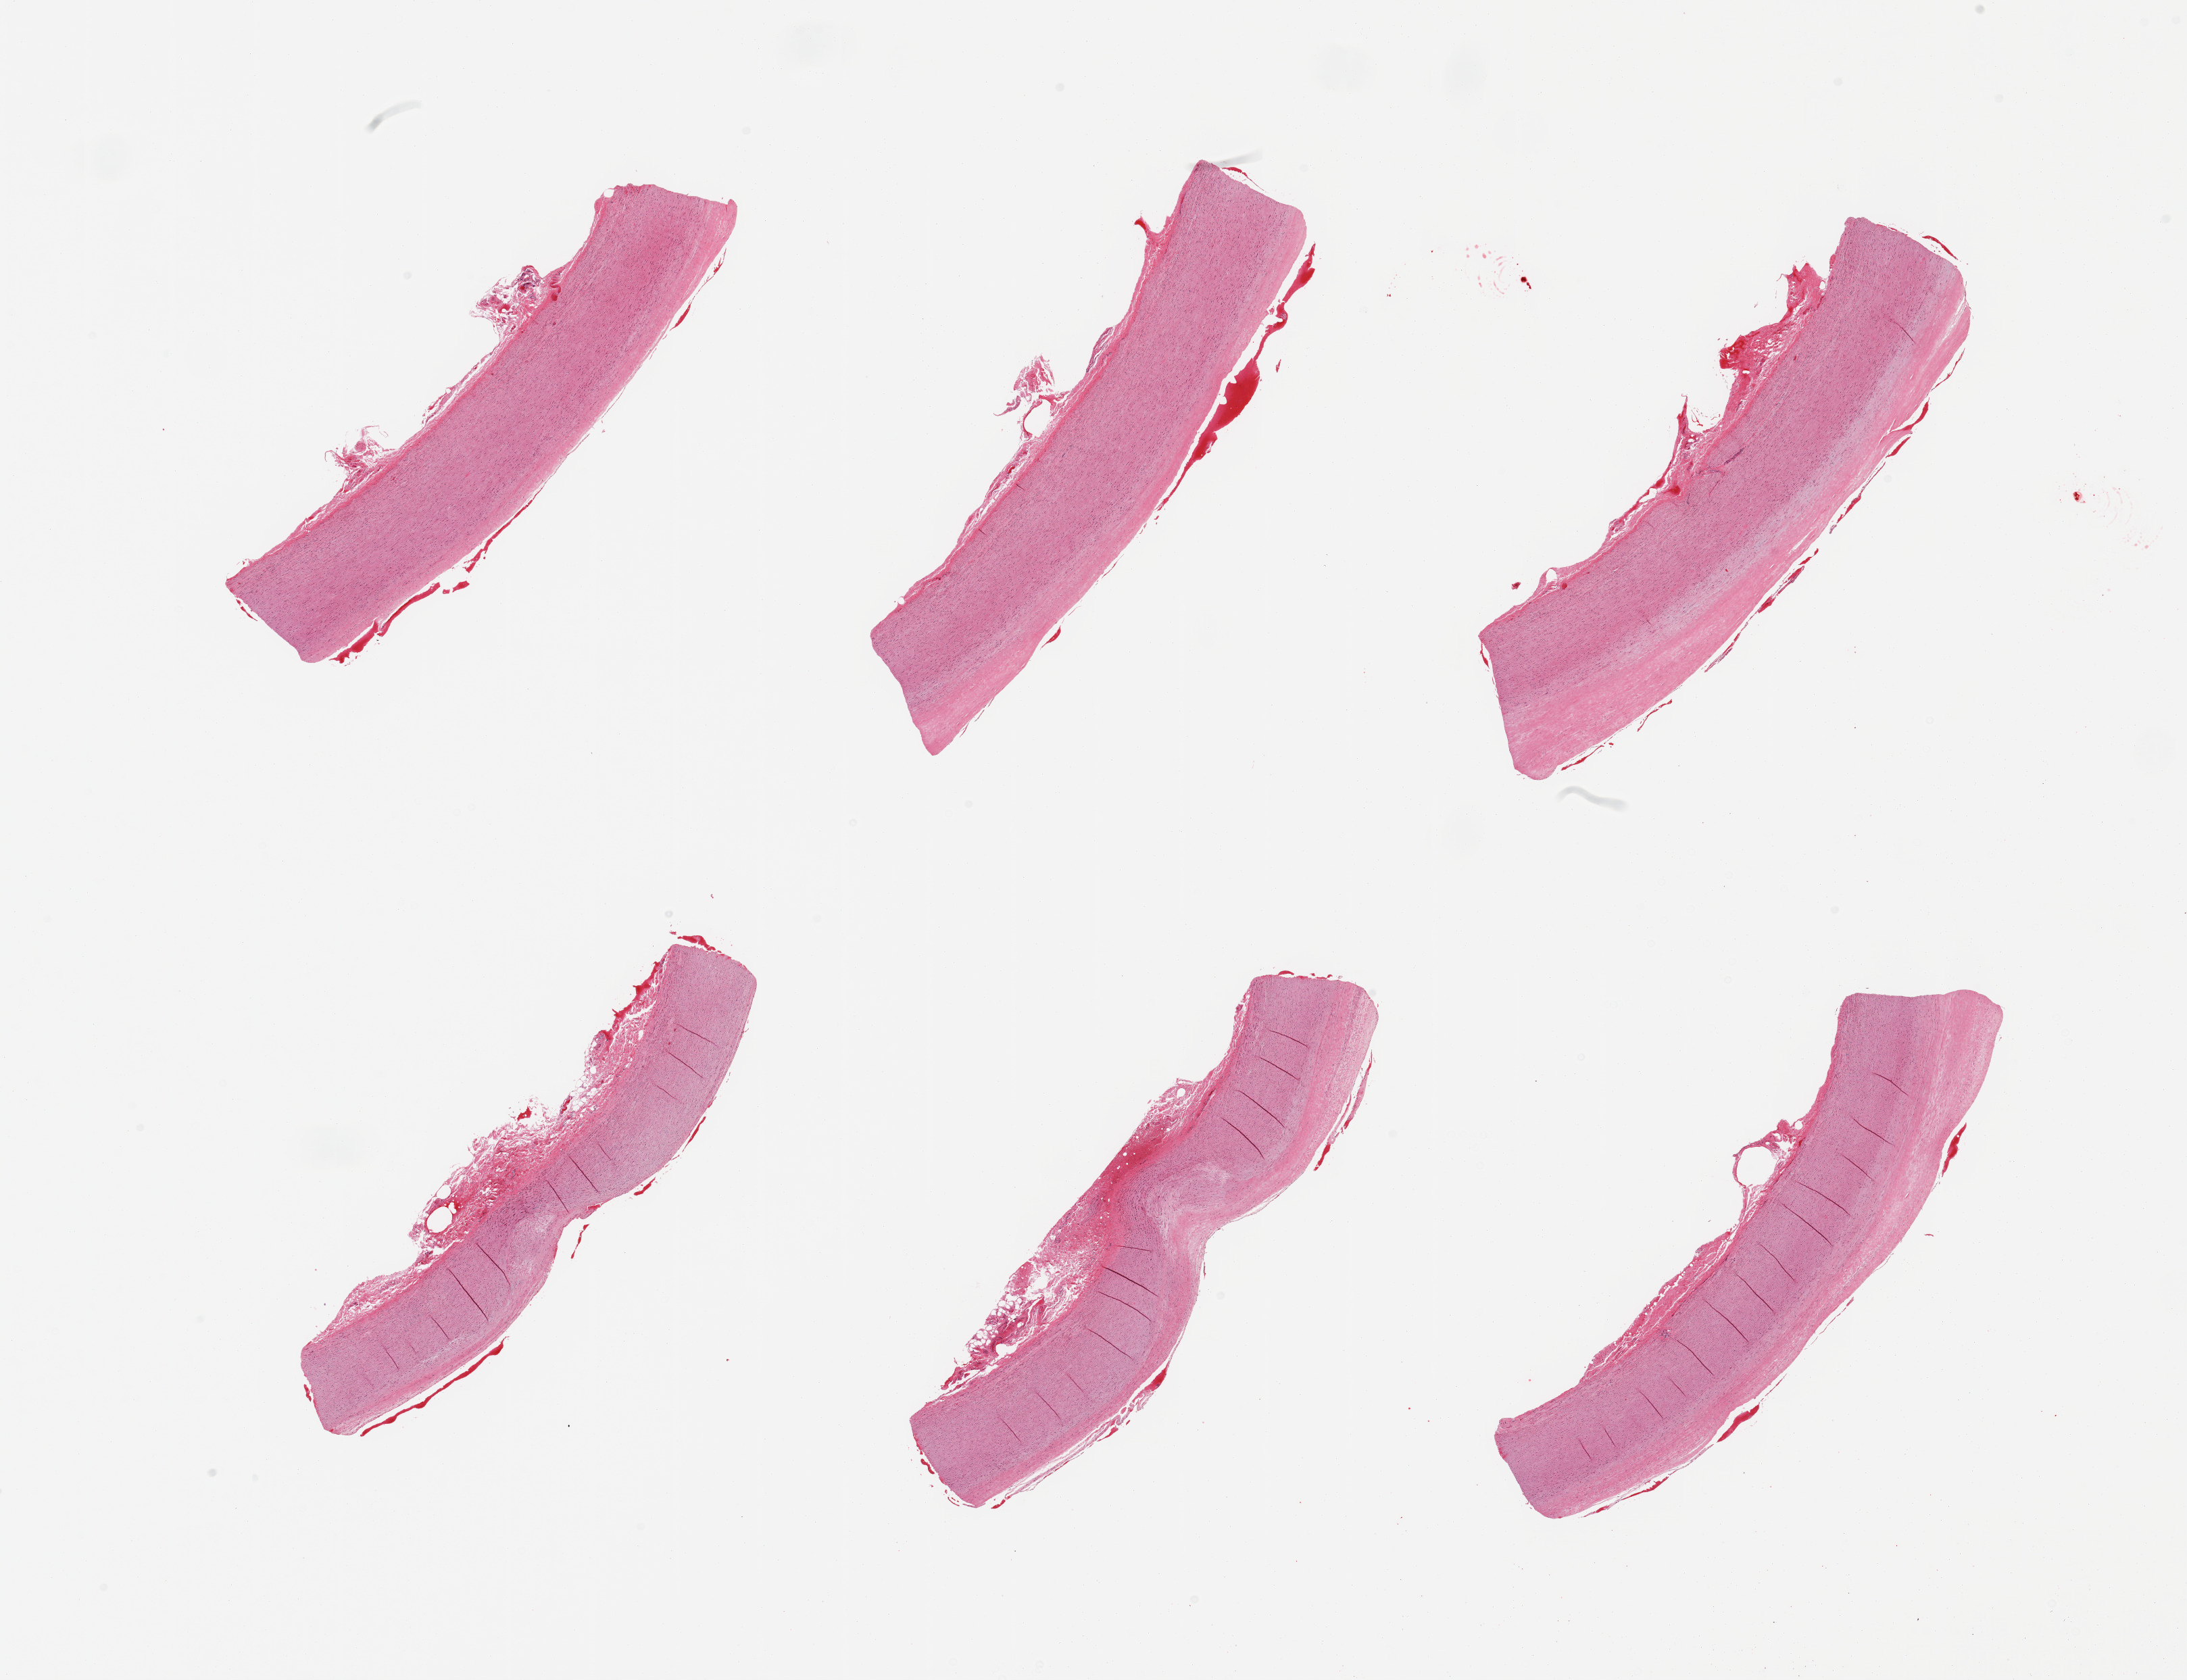
Digitized hematoxylin and eosin (H&E)-stained section, brightfield, shown as a low-resolution overview of the whole scanned area (about 25.6 x 19.7 mm); PAXgene-fixed paraffin-embedded (PFPE) section; sampled site (target tissue): aorta; donor tissue sample. Male donor.
Reviewer comment on this tissue sample: 6 pieces; fine mural fibrosis; flat intimal plaques.